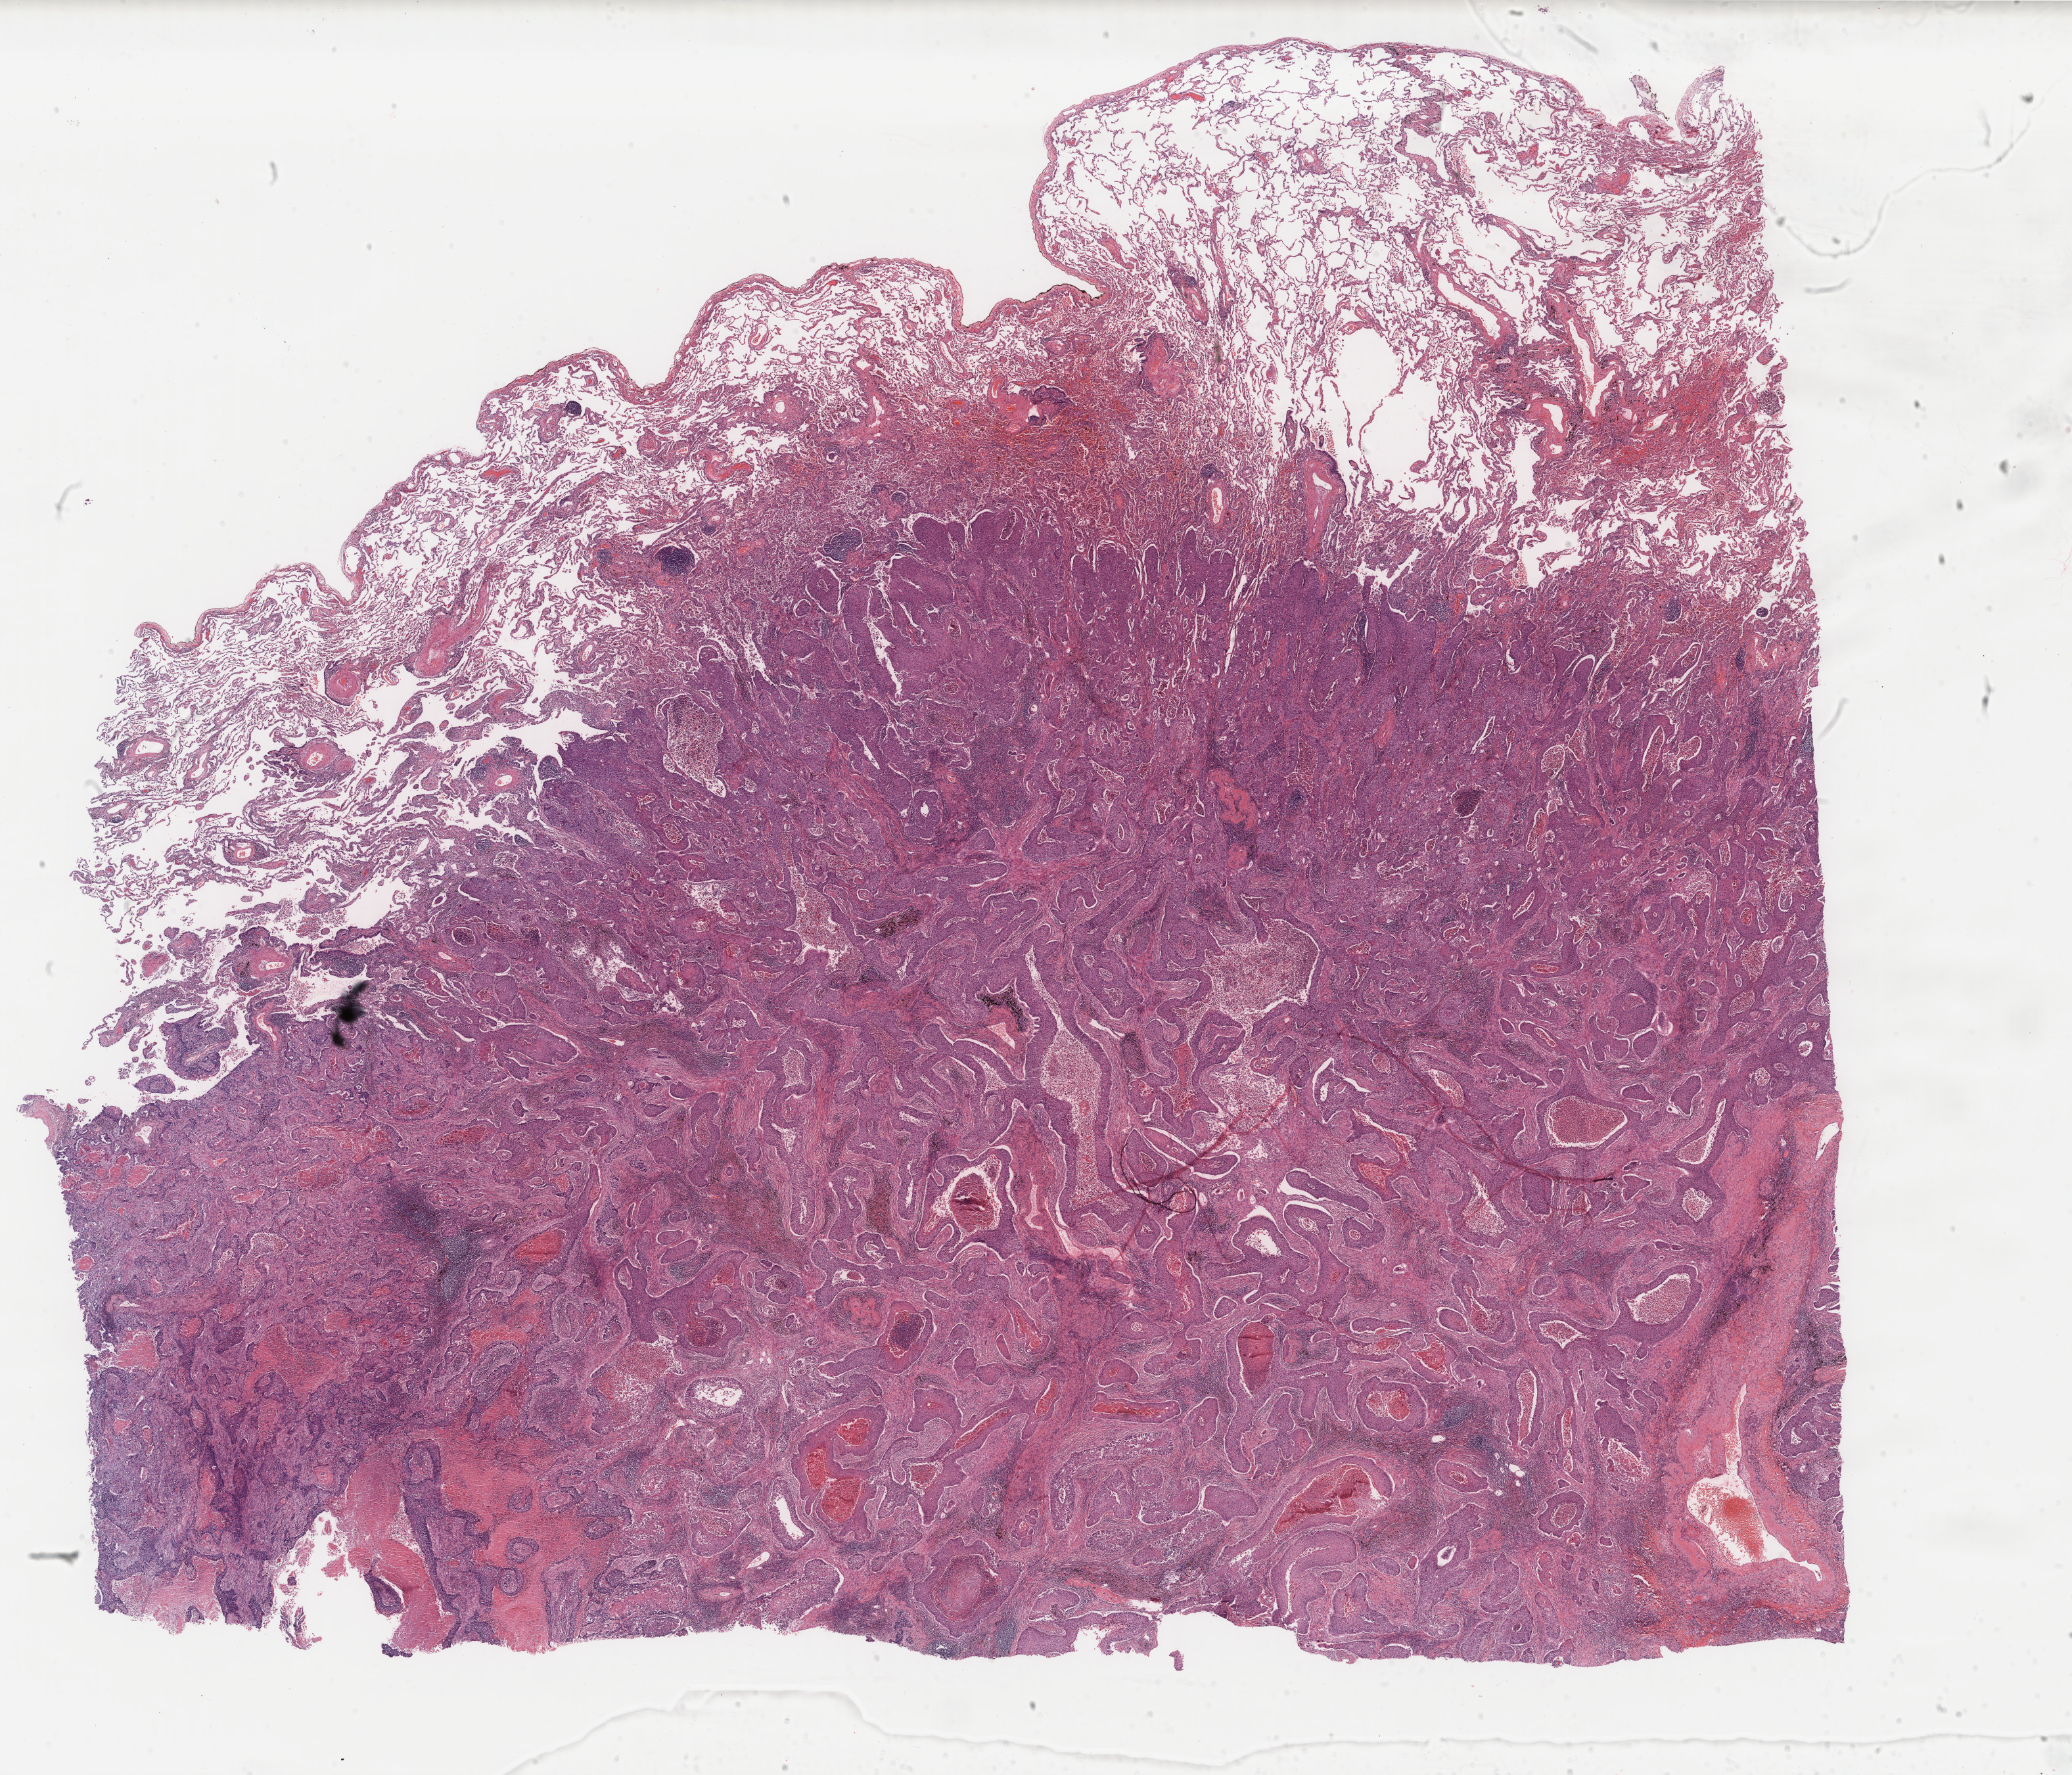
Digitized Hematoxylin and eosin (H&E) stained tissue section (whole slide), whole scanned area (about 25.0 x 21.4 mm, from a 40x scan) shown as a low-resolution overview. Formalin-fixed paraffin-embedded (FFPE) diagnostic section. Lung, primary tumour sample. Male, age 76 years at initial diagnosis.
- pathologic diagnosis: Squamous cell carcinoma, NOS
- AJCC pathologic stage: IB